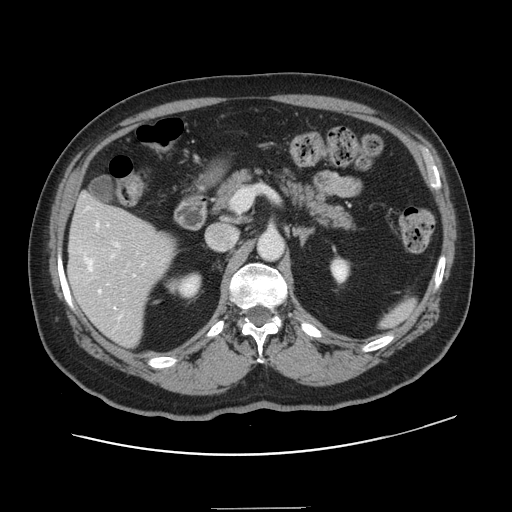
Contrast-enhanced abdominal CT, one axial slice. Slice 74 of 143 in the series (ordered by position). Intravenous contrast given. Soft-tissue window (W 400 / L 40 HU). 512 × 512 image matrix, field of view 402 × 402 mm. Male patient, age 62 years. From the clinical record (not read from this slice): diagnosis: colorectal cancer liver metastases, imaged before liver resection; multiple liver metastases: yes; largest metastasis: 2.7 cm.
Annotated regions visible in this slice (manually delineated by an expert):
- hepatic veins: box from (x=85, y=207) to (x=144, y=320) px
- liver: (x=69, y=196)–(x=175, y=346)
- planned liver remnant (the part of the liver to remain after resection): (x=74, y=196)–(x=130, y=224)
- portal vein (with intrahepatic branches): (x=111, y=242)–(x=120, y=258)